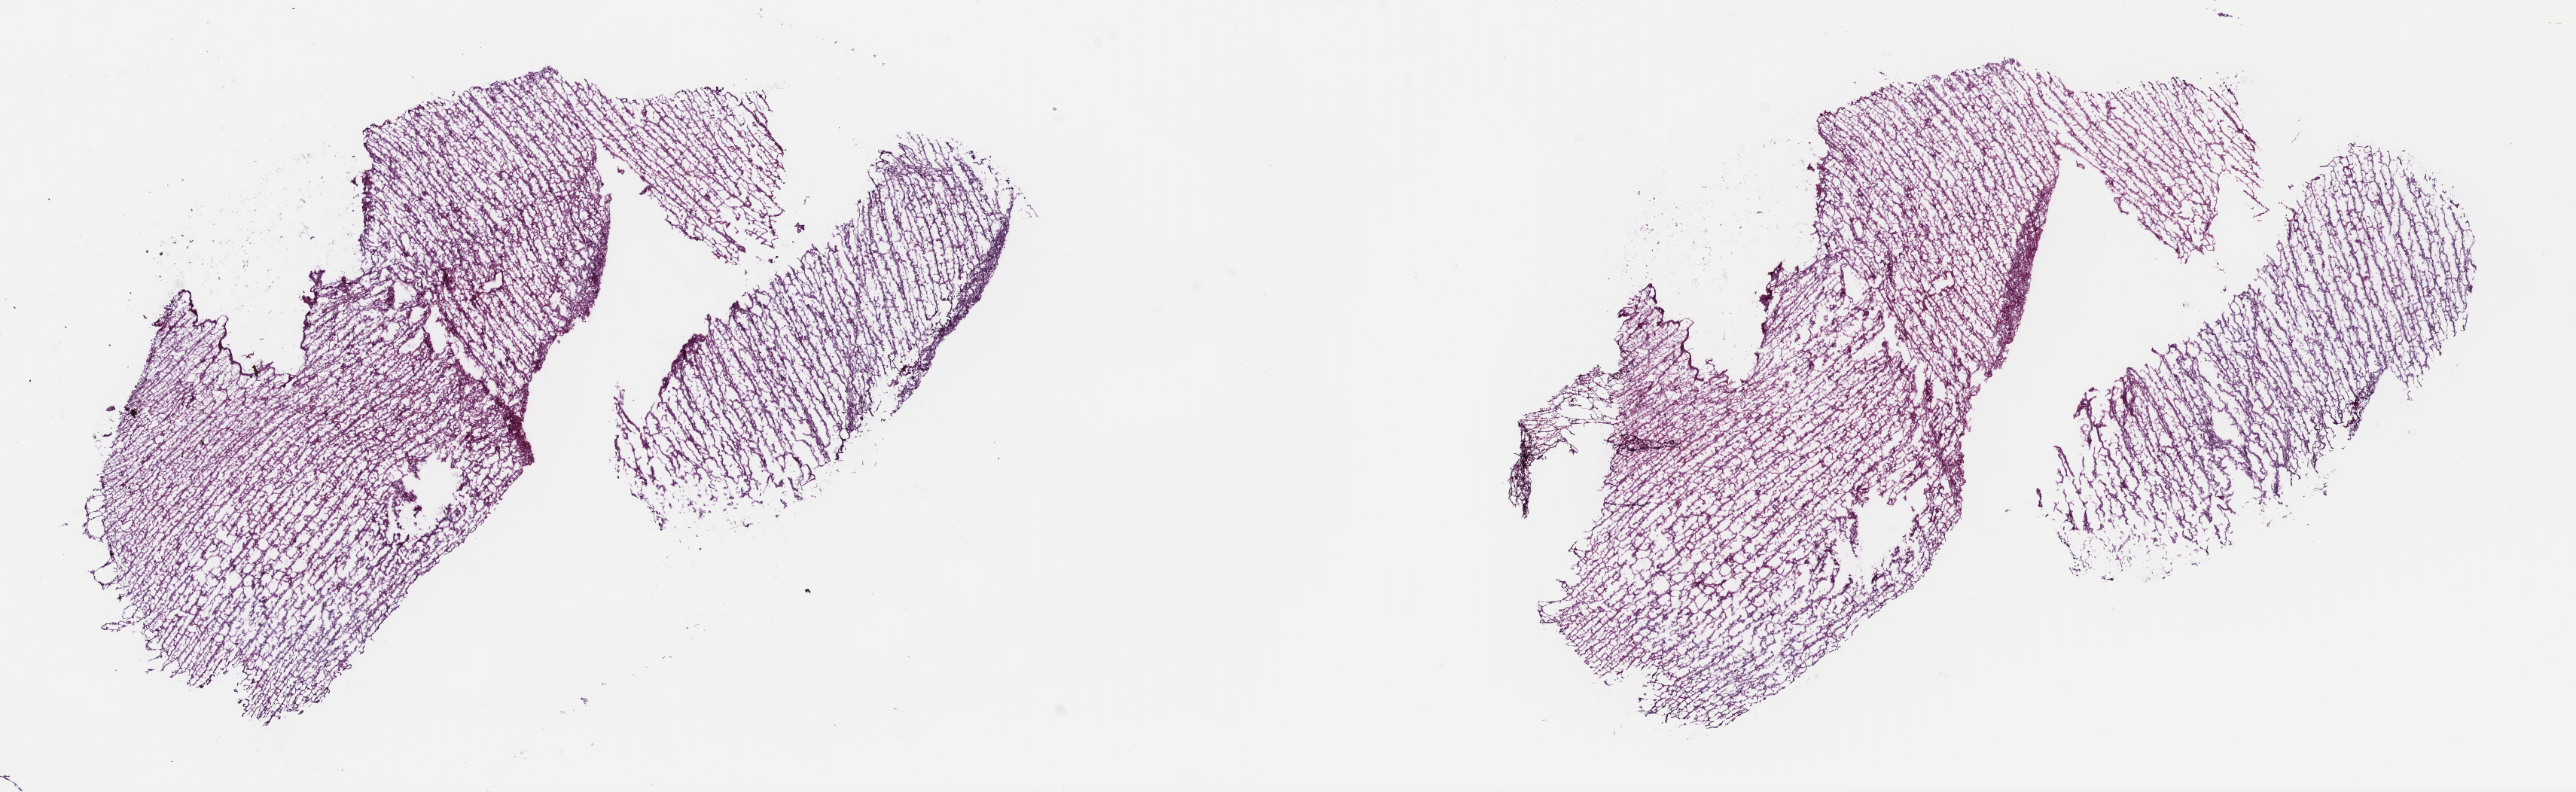
Whole-slide histology image, H&E — shown as a low-resolution overview of the whole scanned area (about 26.9 x 8.3 mm, acquisition: 40x scan); frozen section; brain, primary tumour sample. Male patient; age at initial diagnosis 47 years. Histologic grade: G2 (moderately differentiated). Composition of this section per pathologist review: tumour cells 40%, tumour nuclei 70%, normal cells 10%, stromal cells 50%, necrosis 0%. Inflammatory infiltration, as recorded: lymphocyte infiltration 0%, monocyte infiltration 0%, neutrophil infiltration 0%.
Histologic diagnosis: Astrocytoma, NOS (cerebrum).